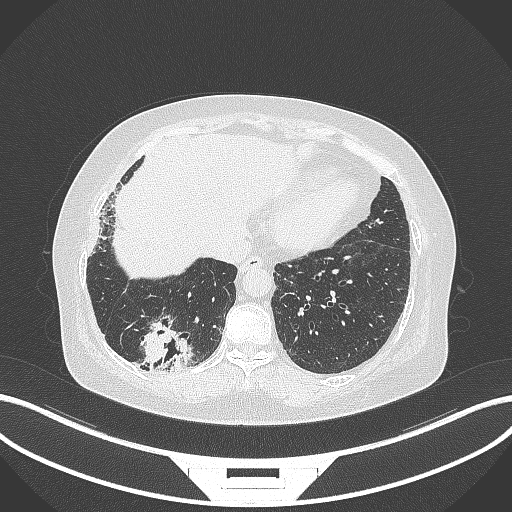
Chest CT, one axial slice. Position 45 of 296 along the scan axis. 120 kVp. Lung window (W 1500 / L -600 HU). 1 mm slice thickness. 512 × 512 image matrix, field of view 400 × 400 mm. Female patient, age 65 years. Case-level facts recorded for this patient, not image findings: clinical TNM (as recorded): T2b N1 M0.
Outlined on this slice (rectangle marked by the reading radiologist):
- lung tumour (recorded histology: adenocarcinoma): bounding box (x1, y1, x2, y2) in pixels: (133, 321, 195, 375)